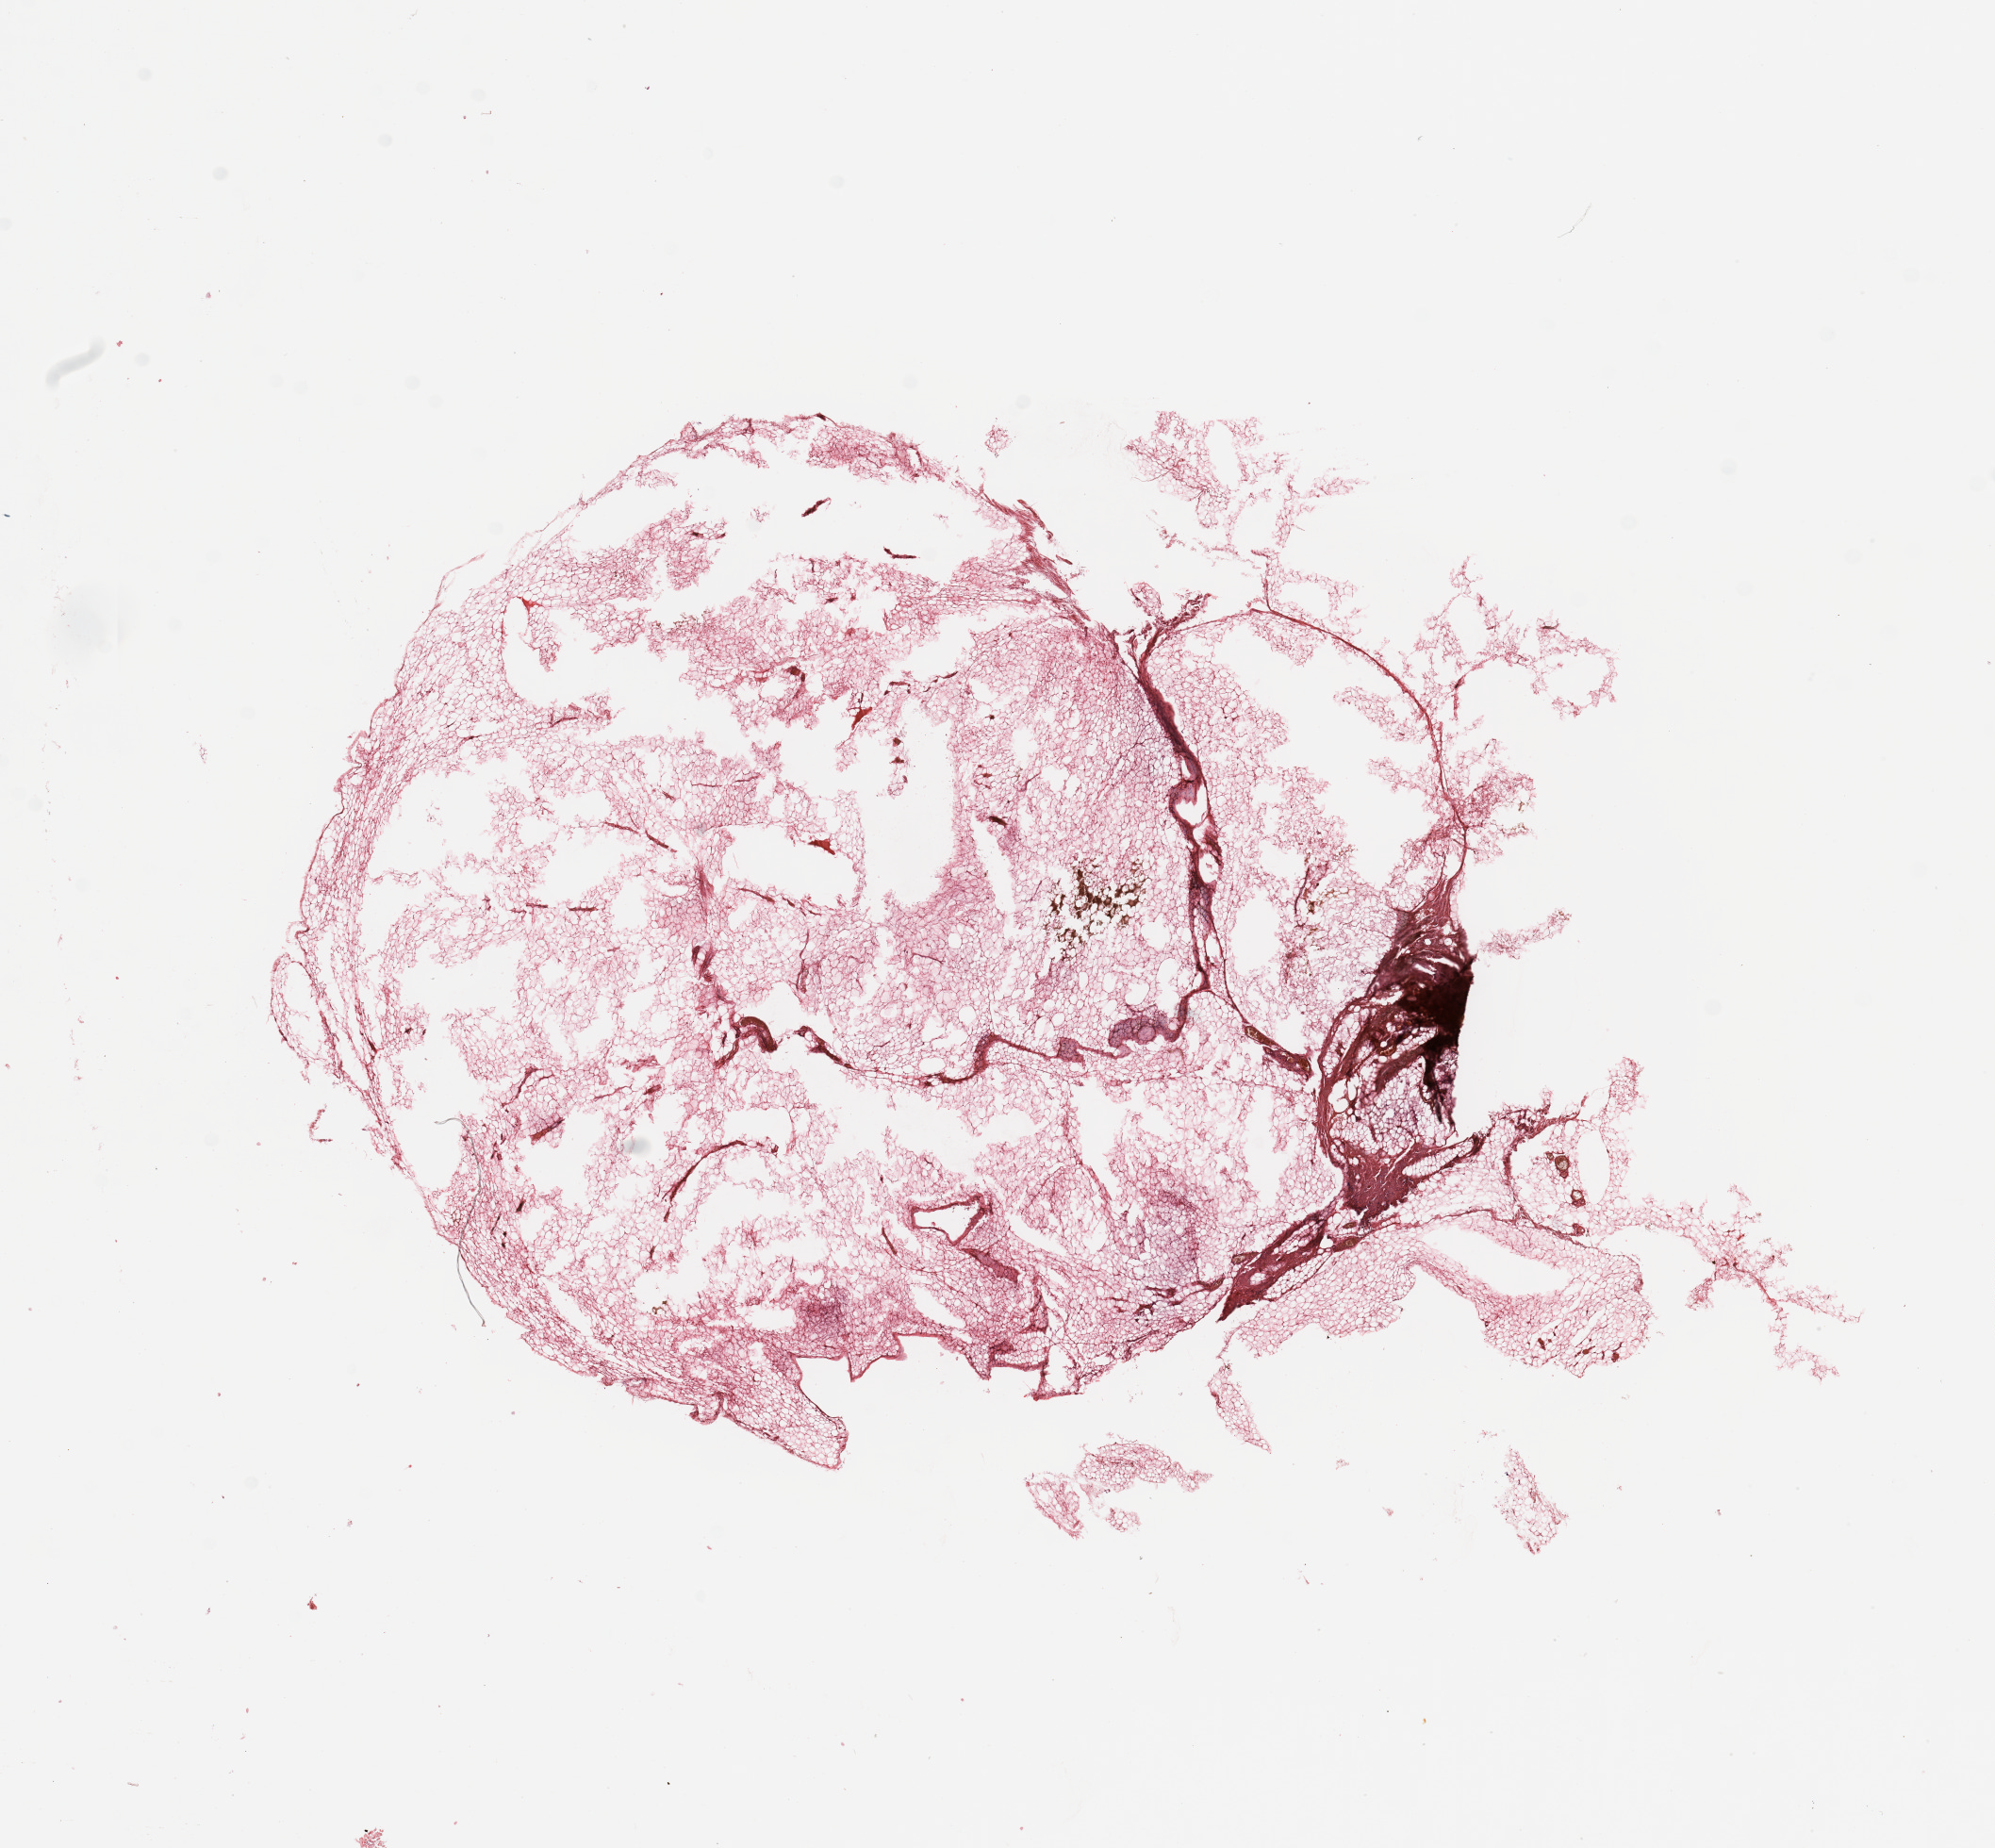
Digitized Hematoxylin and eosin (H&E) stained tissue section (whole slide), a low-resolution overview of the entire scanned area, about 16.7 x 15.5 mm (acquisition: 20x scan). Normal (non-tumour) tissue (melanoma cohort); sampled site not recorded. 74-year-old male patient.
This section: normal (non-tumour) tissue from the same patient. Patient diagnosis (cohort enrolment): cutaneous melanoma (skin).